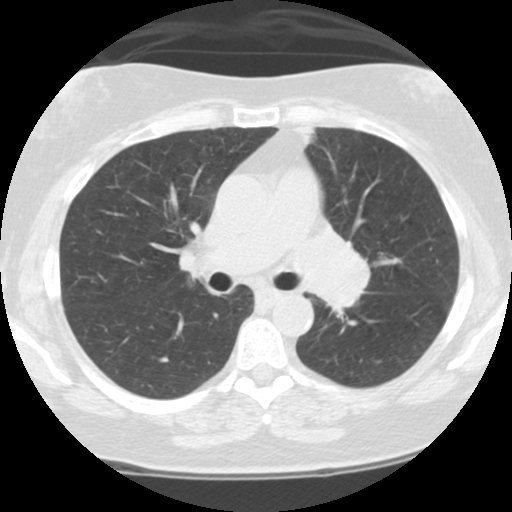
Low-dose screening chest CT, axial slice, third screening round (two years after baseline), lung window (W 1500 / L -600 HU), 2.5 mm slice thickness, slice 43 of 108 in the series, 512 × 512 image matrix, field of view 300 × 300 mm. Female, age 59 years at enrolment. Current smoker at enrolment.
- Expert-annotated lung lesion, box from (x=285, y=213) to (x=386, y=325) px.
- Screening reader's record for this exam: no non-calcified nodule ≥4 mm recorded.
- Official screen result: positive, other.
- Lung cancer was diagnosed 192 days after this screen: small cell carcinoma, NOS, left upper lobe, left hilum, mediastinum, left main stem bronchus, stage IV (AJCC 6th edition), 63 mm at pathology.